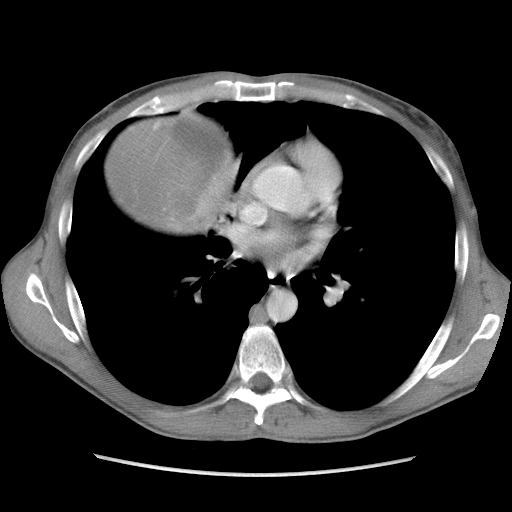
Contrast-enhanced abdominal CT, one axial slice. Slice 104 of 115 in the series (ordered by position). Soft-tissue window (W 400 / L 40 HU). 512 × 512 image matrix, field of view 360 × 360 mm. Male patient. Case-level facts recorded for this patient, not image findings: diagnosis: adrenocortical carcinoma; tumour side: right adrenal; Ki-67 index: 13 %; stage (as recorded): 3.
Annotated regions visible in this slice (semi-automatically segmented with operator editing):
- mass: bounding box (x1, y1, x2, y2) in pixels: (108, 116, 230, 234)